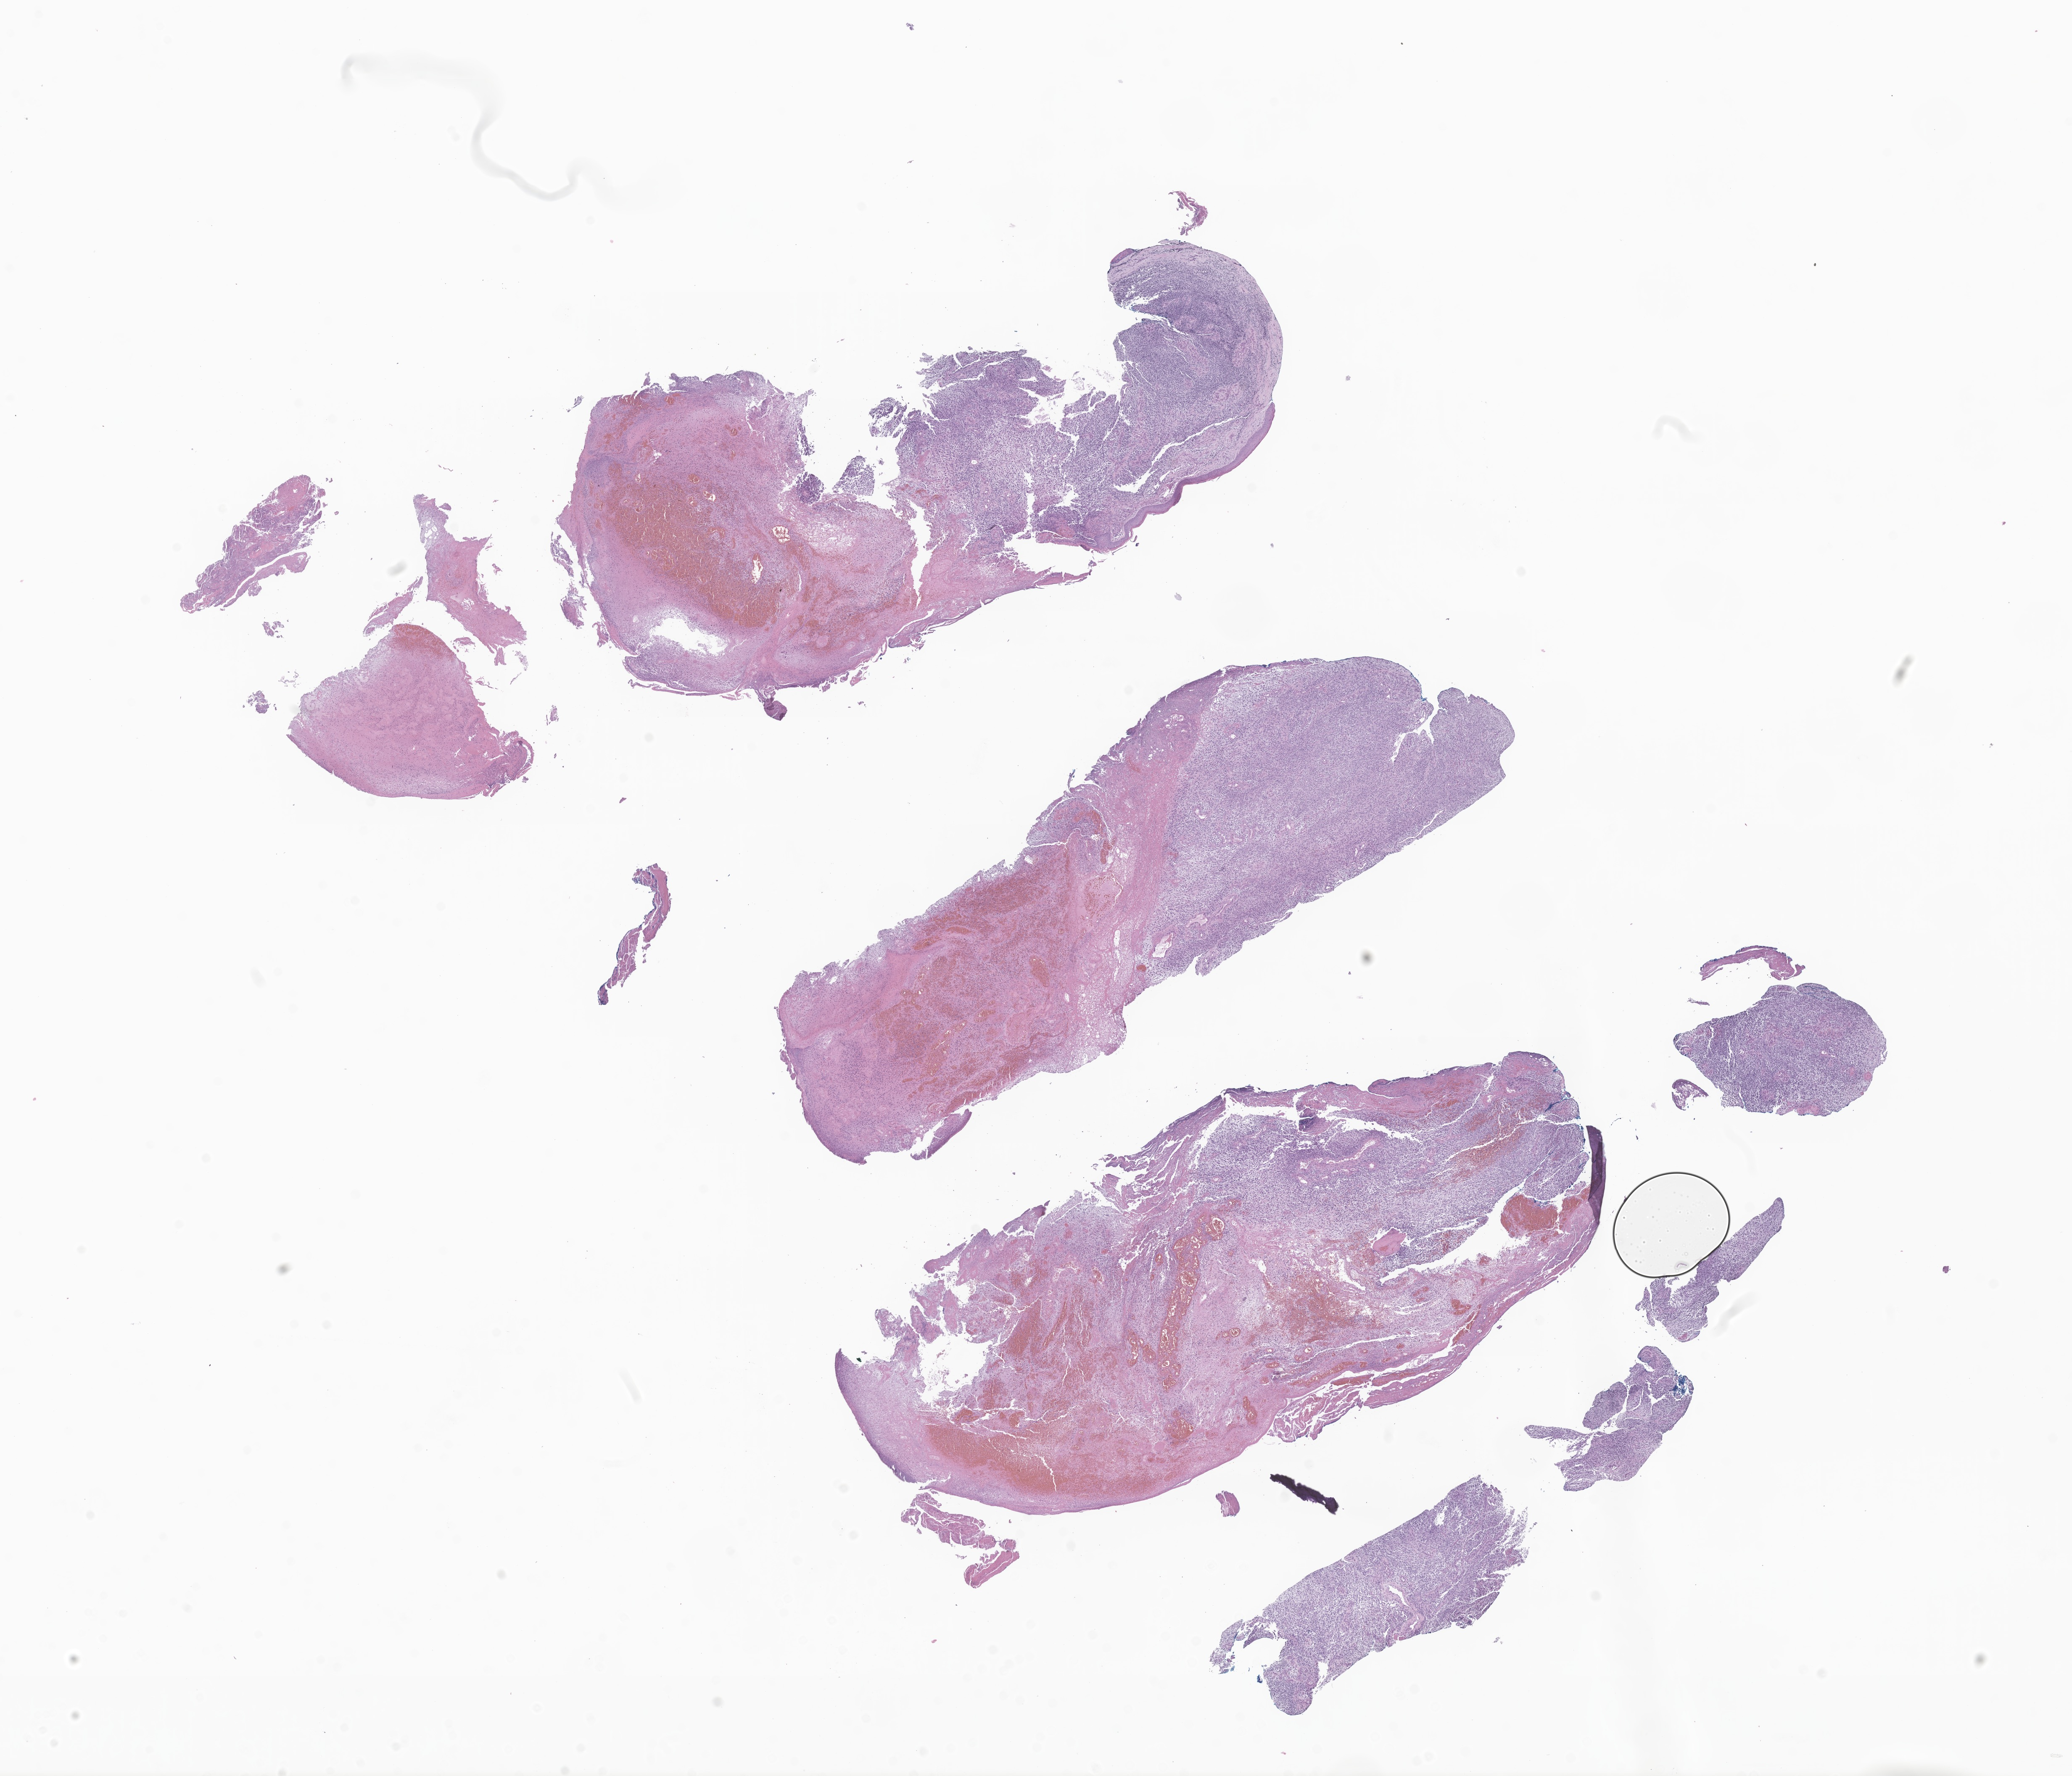
Whole-slide image, H&E stain of tumor tissue from the middle ear, whole scanned area (about 20.8 x 17.8 mm) shown as a low-resolution overview, FFPE section. Male patient, age 635 days.
Diagnosis (ICD-O-3 morphology term): Embryonal rhabdomyosarcoma, NOS.